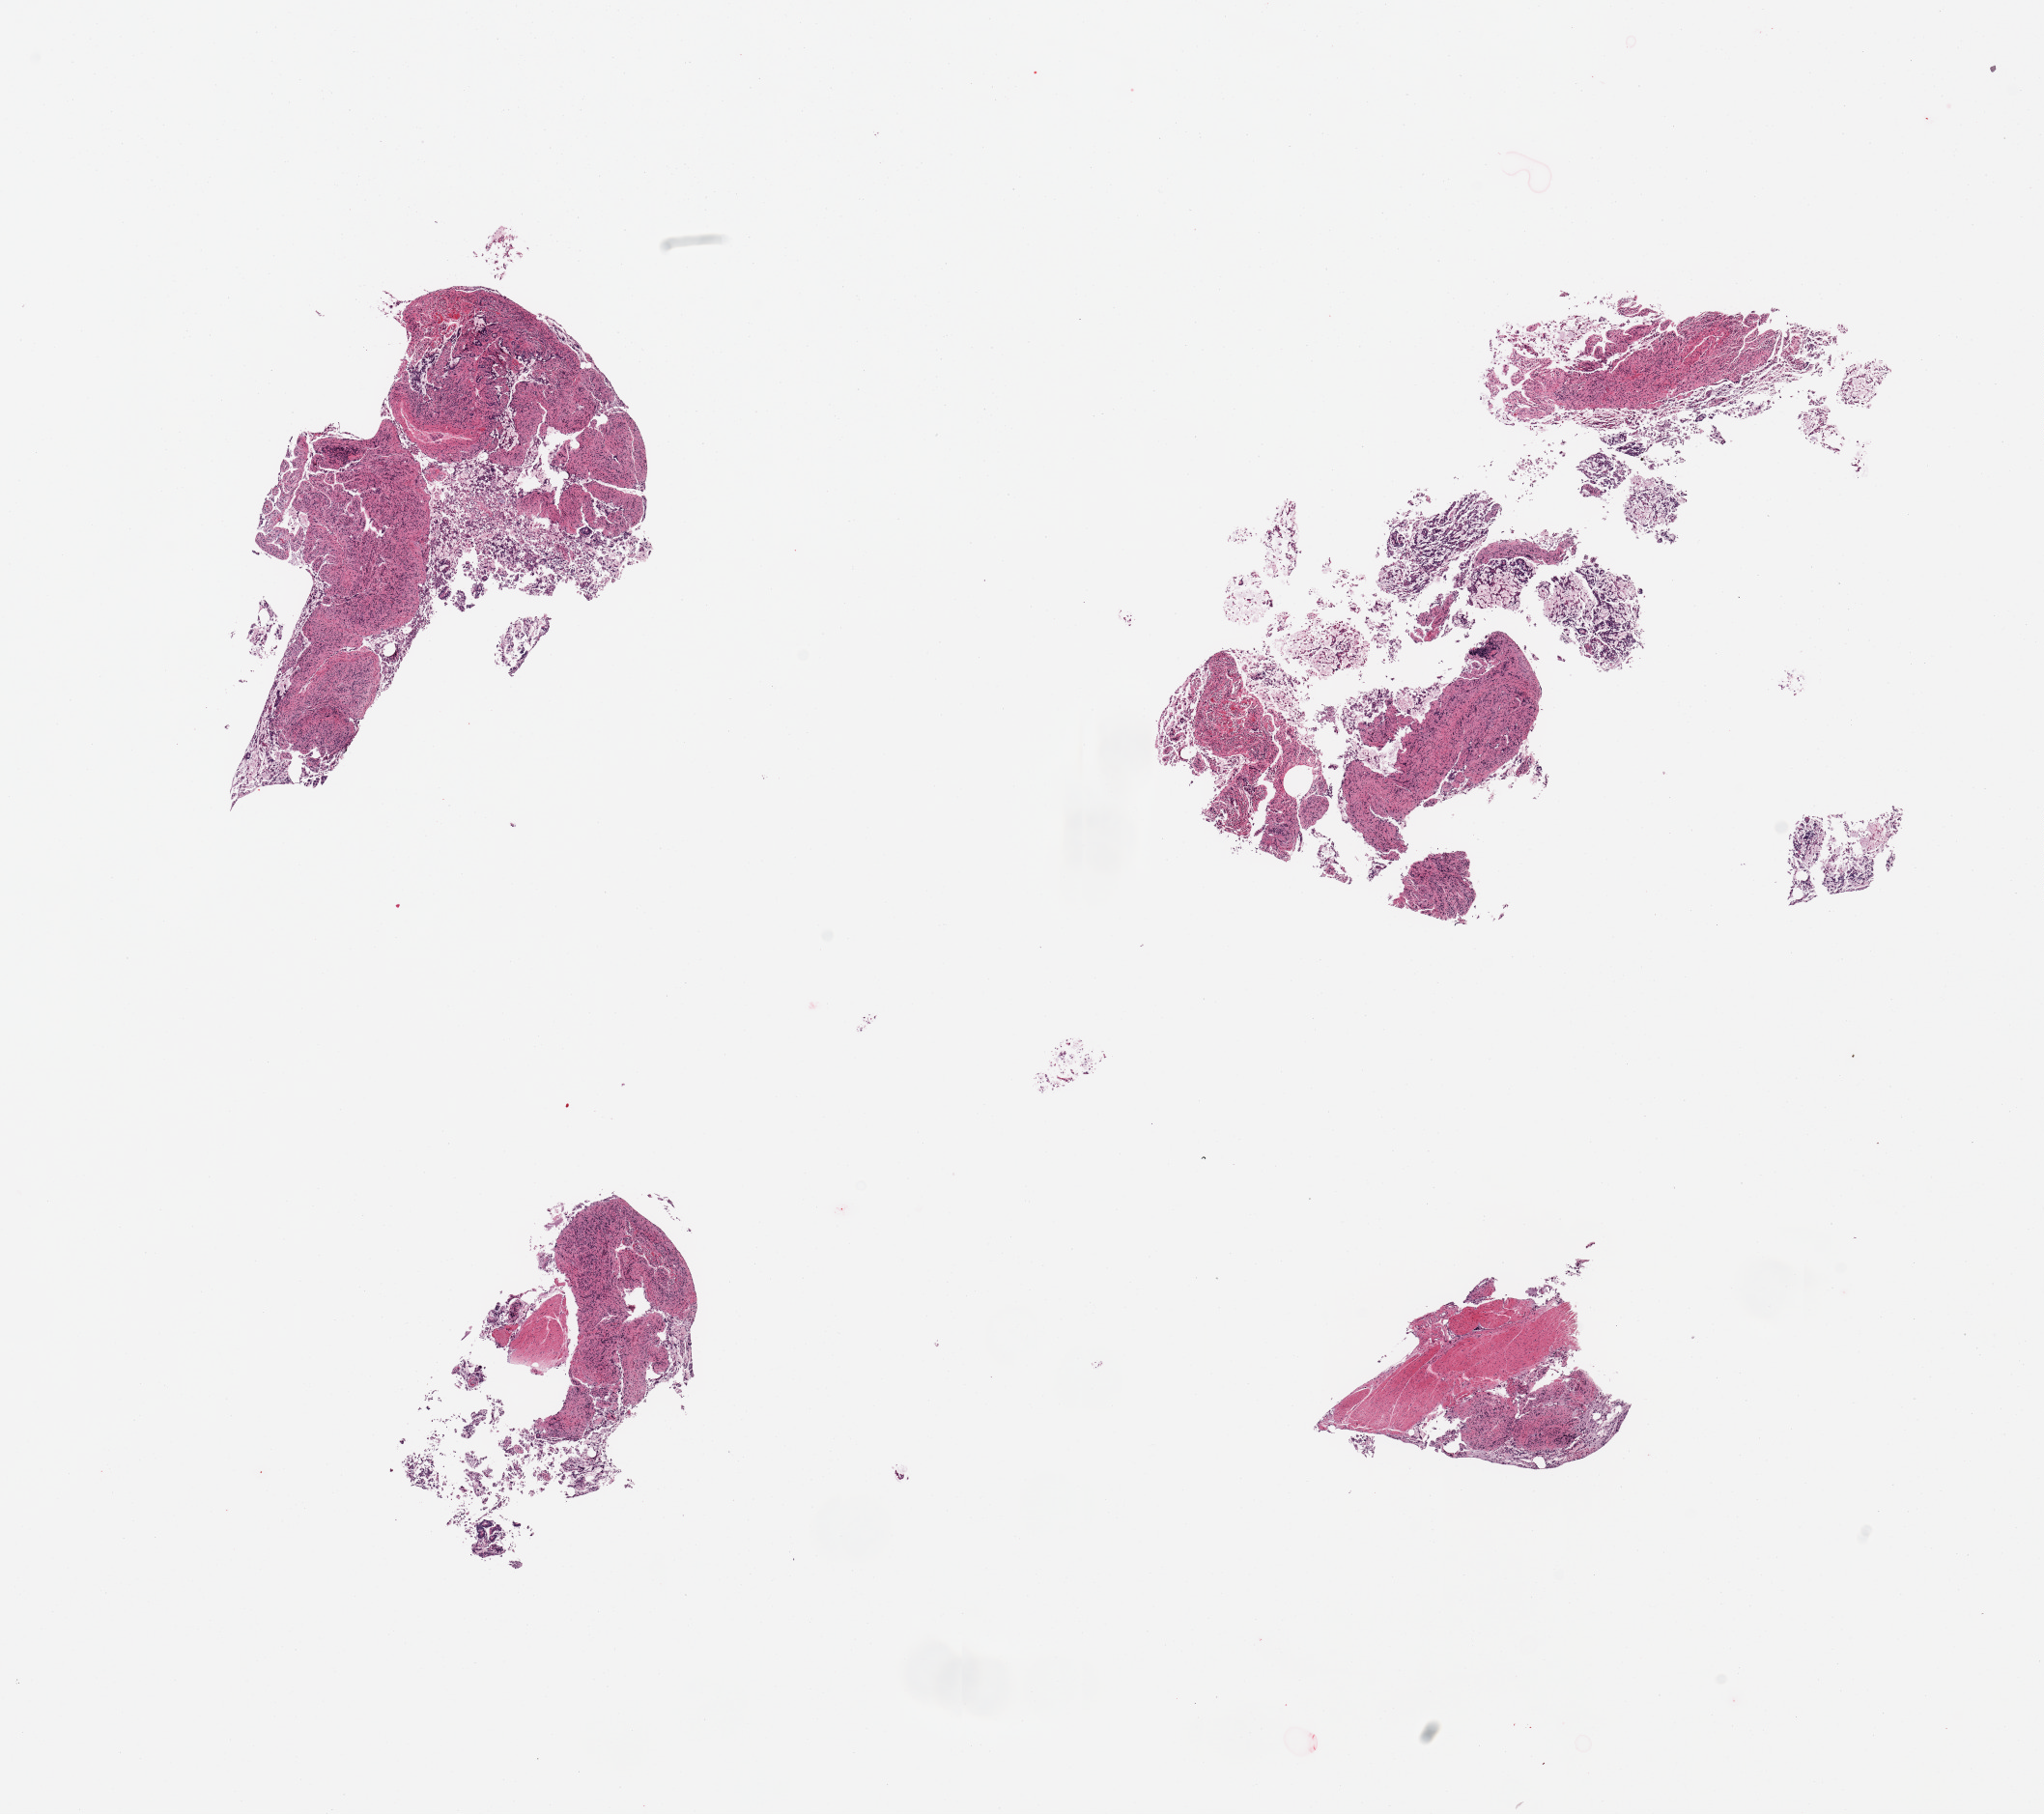
Digitized hematoxylin and eosin (H&E)-stained section, brightfield — a low-resolution overview of the entire scanned area, about 16.7 x 14.9 mm (from a 20x scan); PAXgene-fixed, paraffin-embedded tissue; section of ileum (target tissue); tissue donor sample.
Review note (as recorded): 4 pieces, autolyzed mucosa, insufficient viable lymphoid aggregates to warrant analysis.